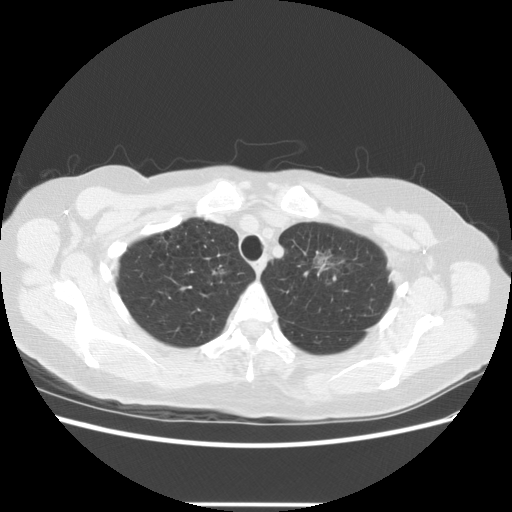
Axial slice from a low-dose chest CT screening exam; third annual screen; lung window (W 1500 / L -600 HU); slice 104 of 126 in the series. Female participant, aged 65 years at enrolment. Former smoker at enrolment.
Lesion marked by an expert reader, box from (x=291, y=230) to (x=366, y=294) px. Reader record for this screening exam (exam-level; its link to the box is not recorded): non-calcified nodule or mass ≥4 mm, left upper lobe, 17 × 14 mm, poorly defined margins, ground glass attenuation, pre-existing on the prior screen: yes; interval growth: yes. Official screen result: positive, other. Lung cancer was diagnosed 96 days after this screen: adenocarcinoma, NOS, left upper lobe, moderately differentiated (G2), stage IA (AJCC 6th edition), 30 mm at pathology.